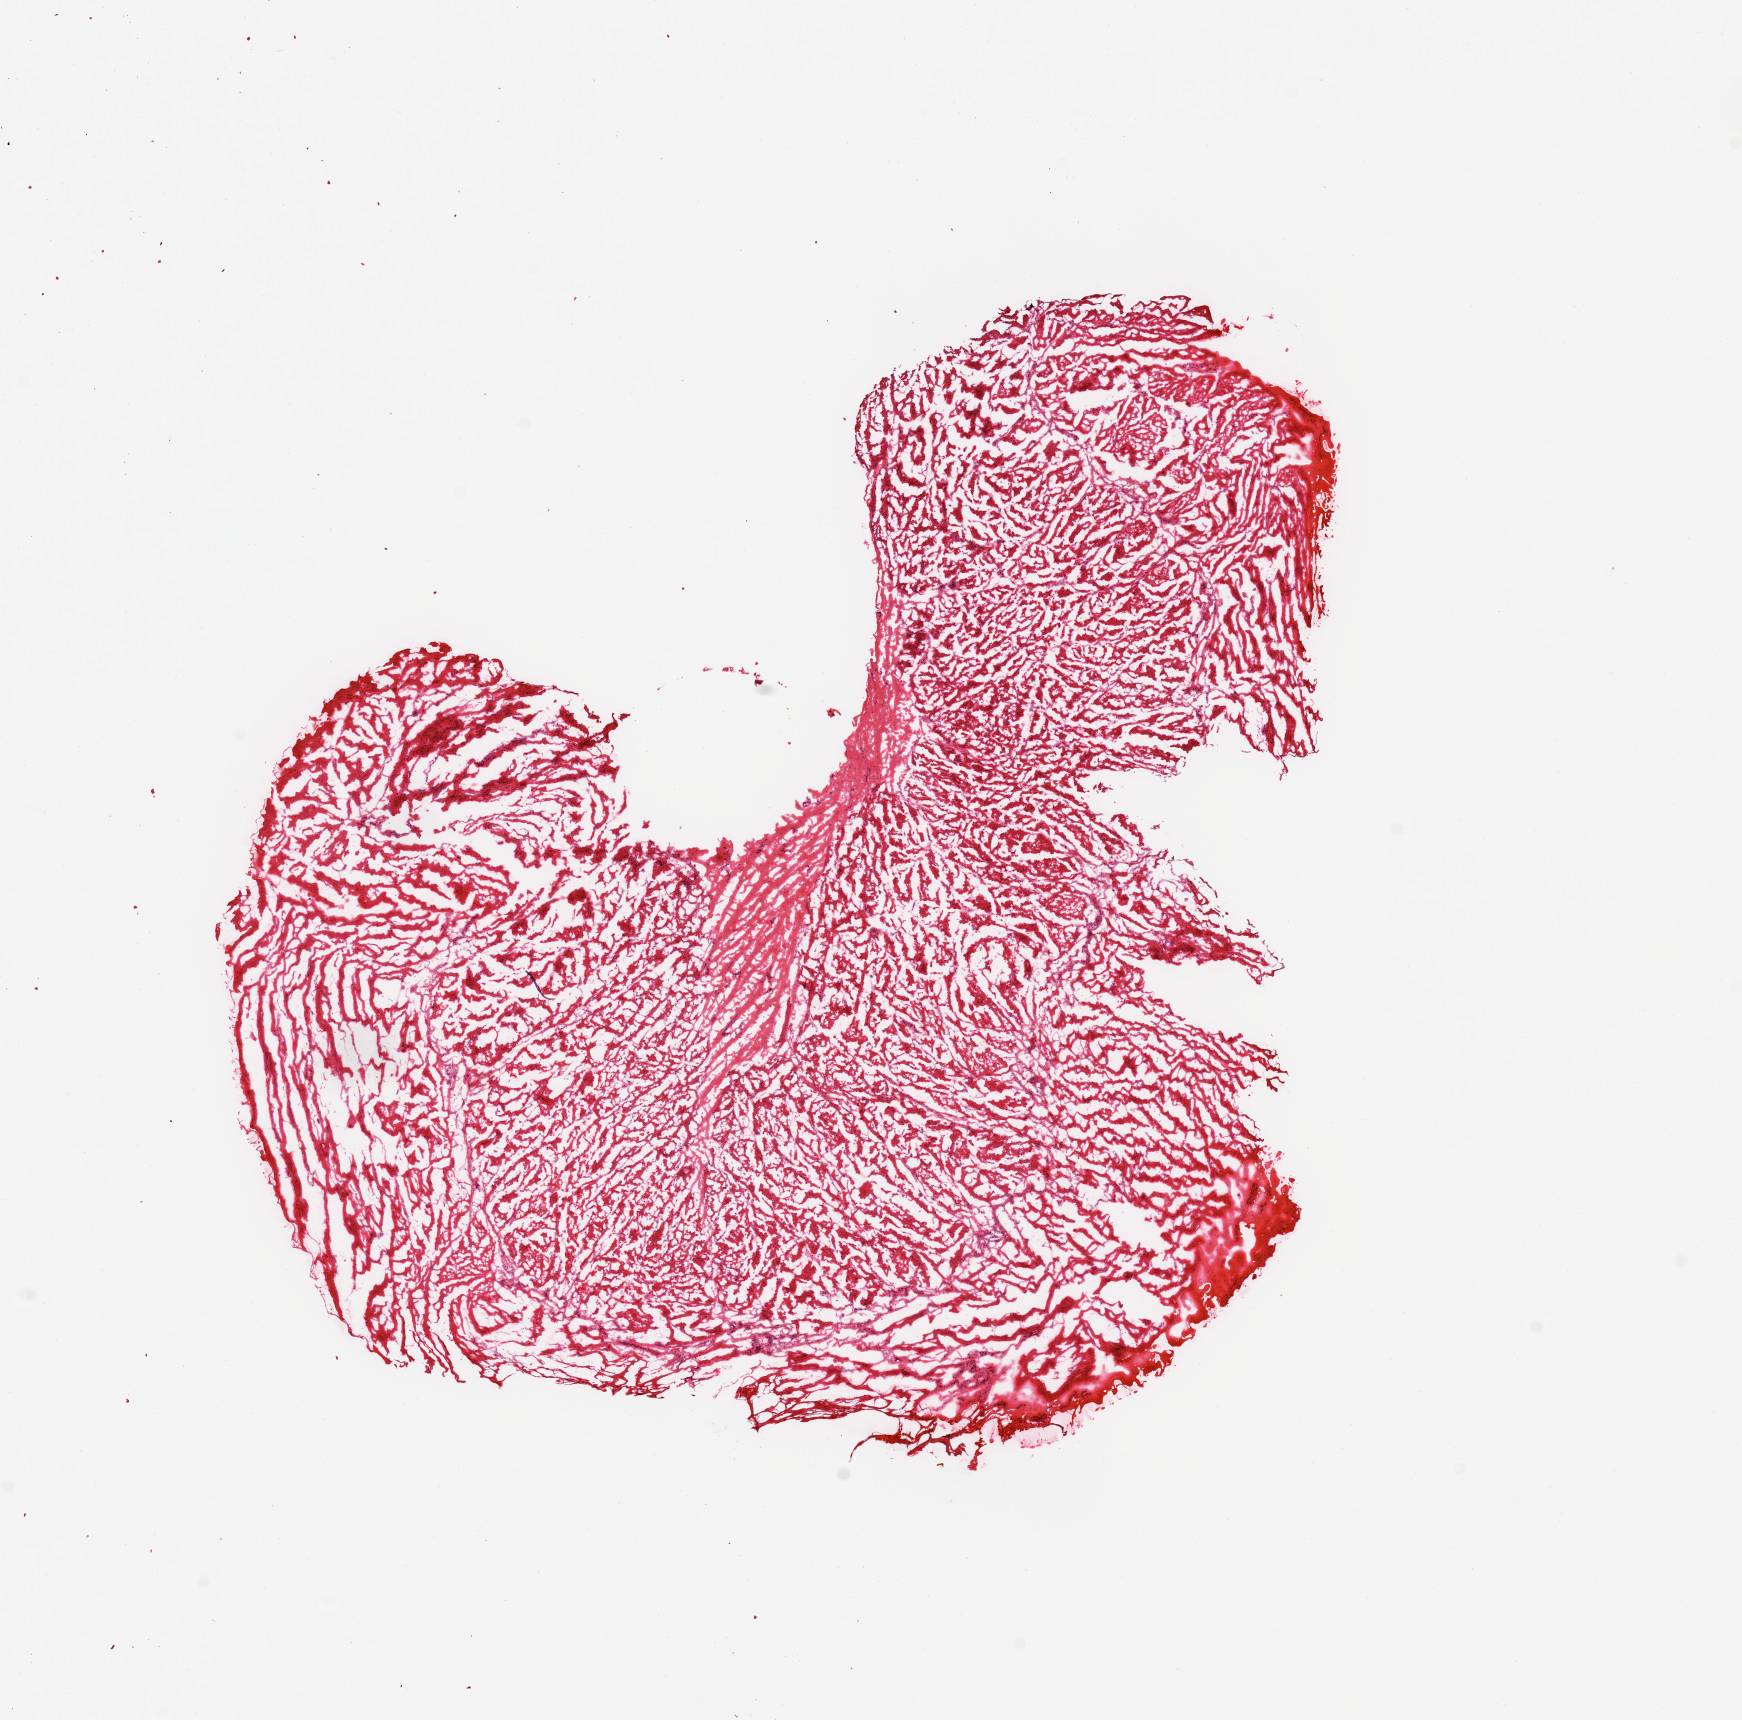
Whole-slide image, hematoxylin and eosin (H&E) stain — shown as a low-resolution overview of the whole scanned area (about 13.8 x 13.6 mm). Donor sex: male.
Specimen: frozen section; section of prostate (target tissue); donor tissue sample.